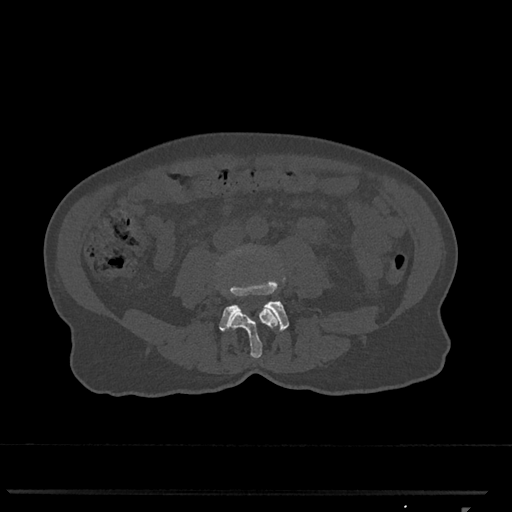
CT including the spine, one axial slice. Position 239 of 793 along the scan axis. Reconstruction kernel Br40s/3. 120 kVp. Bone window (W 1800 / L 400 HU). 0.5 mm slice thickness. 512 × 512 image matrix, field of view 380 × 380 mm. Female patient, age 62 years. Case-level facts recorded for this patient, not image findings: primary cancer: renal.
Structures marked on this image (semi-automatic segmentation, software-assisted and operator-edited):
- L3 vertebra: bounding box <226,249,280,358> (left, top, right, bottom; pixels)
- L4 vertebra: <219,278,289,332>